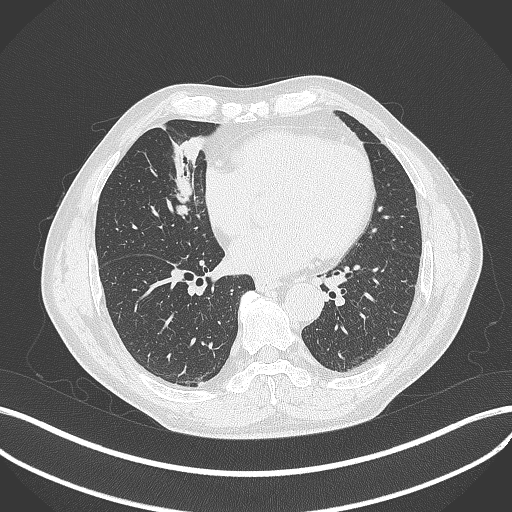
Chest CT, one axial slice. Reconstruction kernel B70f. 120 kVp. Lung window (W 1500 / L -600 HU). 1 mm slice thickness. 512 × 512 image matrix, field of view 400 × 400 mm. Male patient, age 61 years. Case-level facts recorded for this patient, not image findings: clinical TNM (as recorded): T2b N1 M0.
Structures marked on this image (bounding box drawn by a radiologist):
- lung tumour (recorded histology: squamous cell carcinoma): bounding box <165,164,201,213> (left, top, right, bottom; pixels)